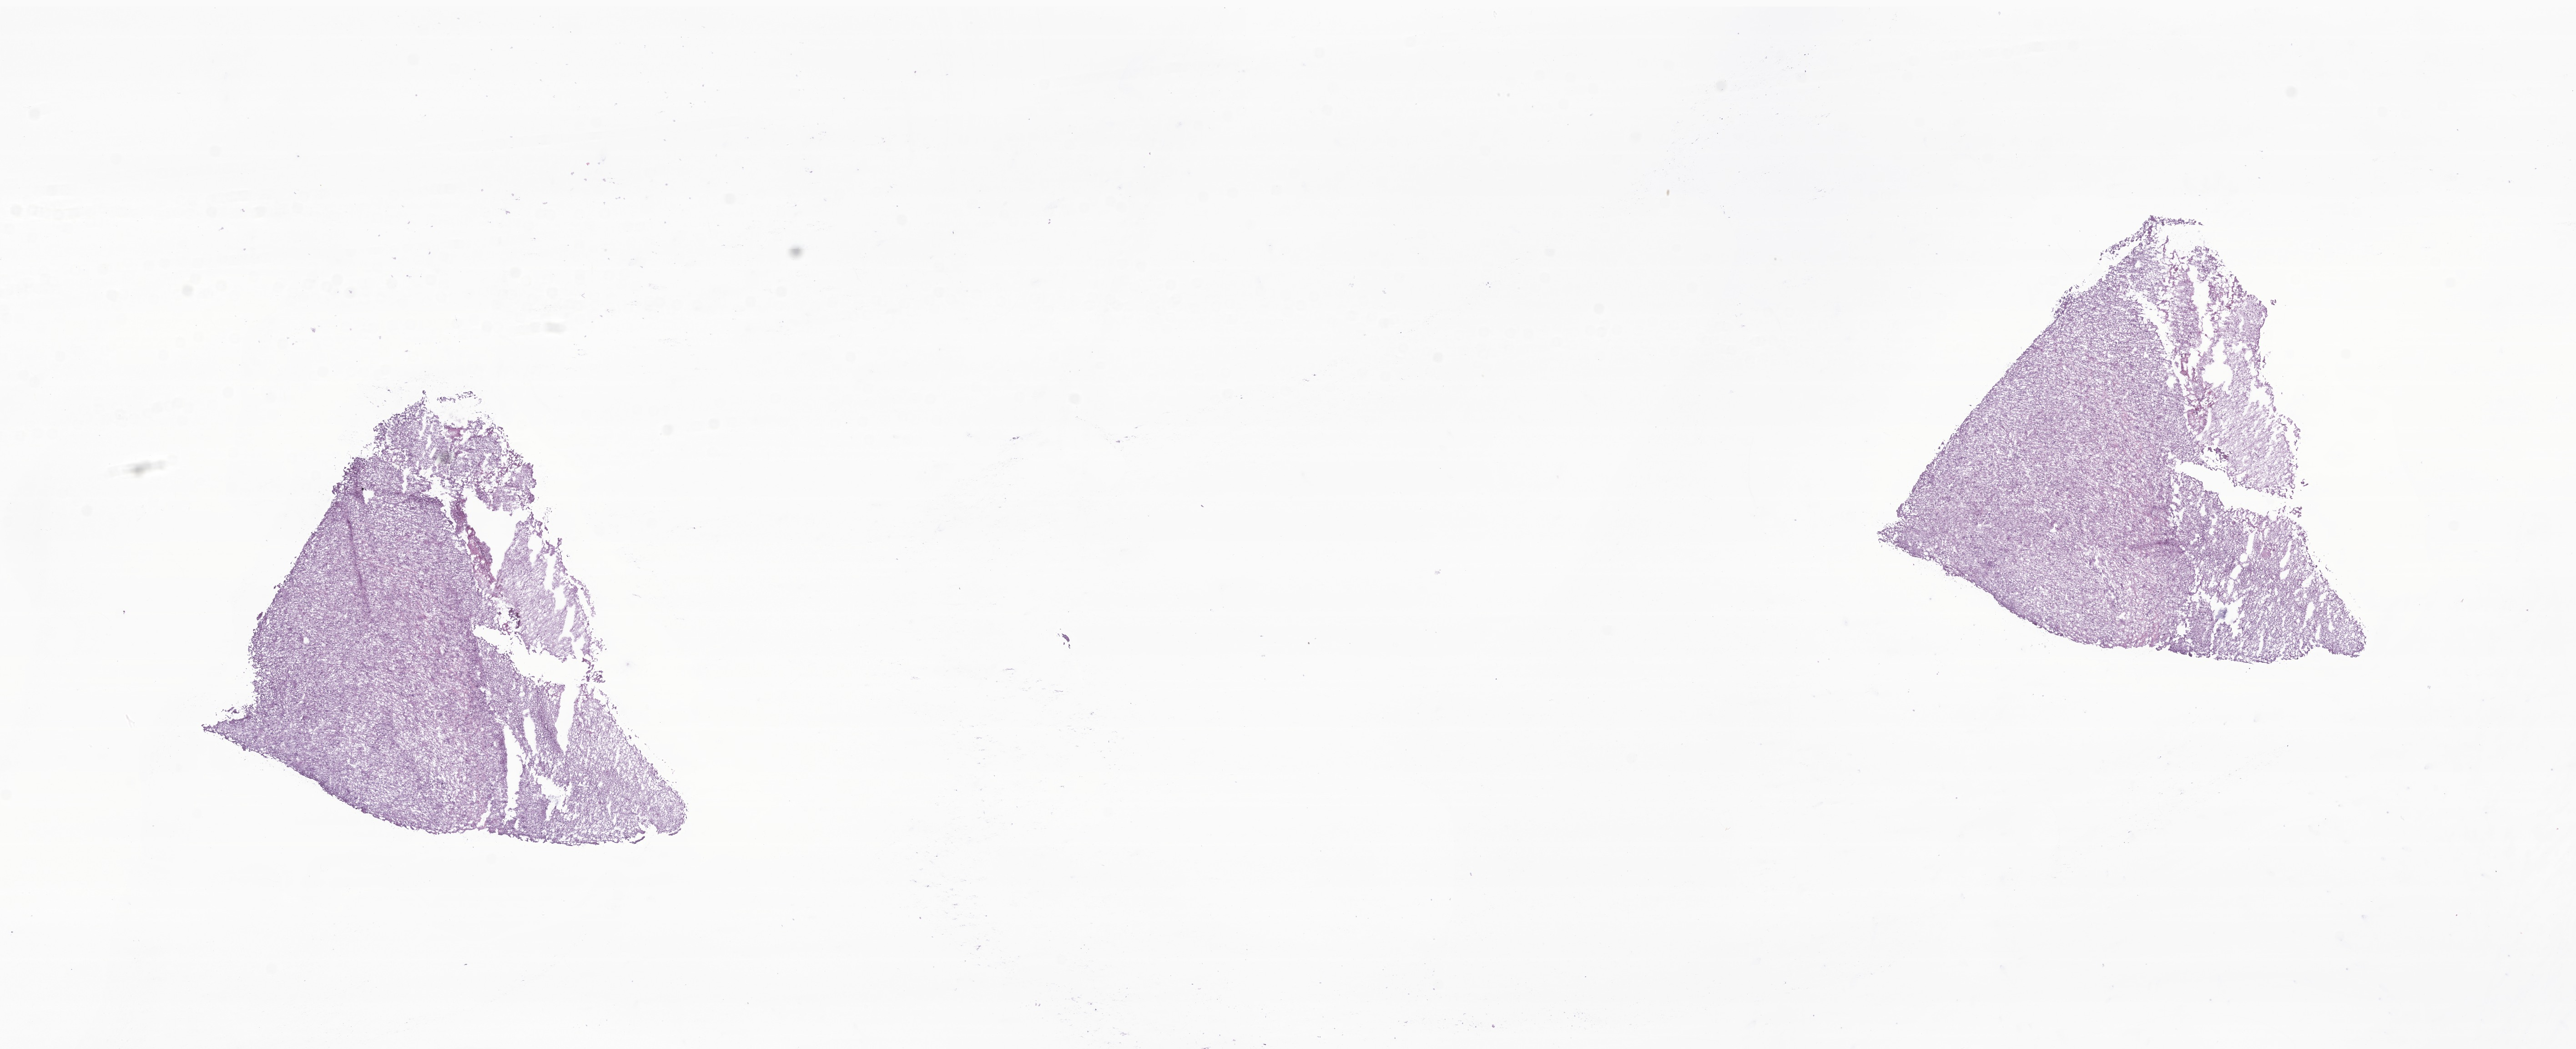
Whole-slide image, hematoxylin and eosin (H&E) stain of tumor tissue from the parietal lobe, low-resolution overview of the scanned area, about 23.9 x 9.7 mm, frozen section. Female patient, age 134 months (11 years 2 months).
* recorded diagnosis: Pleomorphic xanthoastrocytoma, NOS